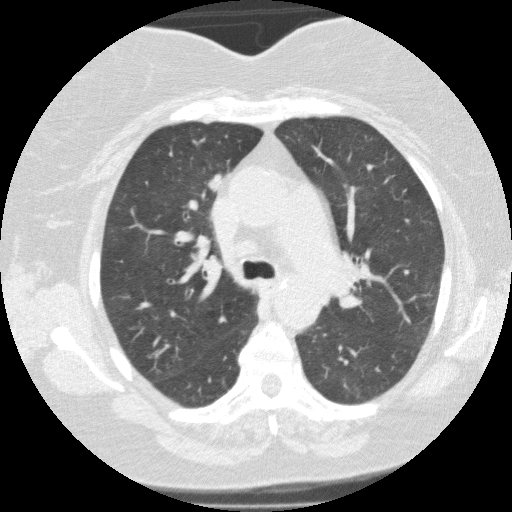
Low-dose screening chest CT, axial slice, third annual screen, lung window (W 1500 / L -600 HU), 2 mm slice thickness, slice 51 of 146 in the series. Female participant, aged 62 years at enrolment. Current smoker at enrolment.
Lesion marked by an expert reader, bounding box (x1, y1, x2, y2) in pixels: (190, 162, 239, 201). The screening reader recorded 5 non-calcified nodules or masses ≥4 mm on this exam (right upper lobe, right lower lobe, right lower lobe, right lower lobe, right lower lobe); which of them this box marks is not recorded. Official screen result: positive, other.